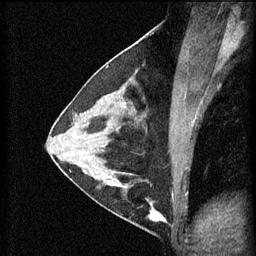
Breast MRI (dynamic contrast-enhanced), one sagittal slice; position 31 of 60 along the scan axis; 3 images stored at this slice position (order not interpretable as contrast timing); 1.5 T; TE 4.2 ms, TR 11 ms; 2 mm slice thickness; 256 × 256 image matrix, field of view 180 × 180 mm. Patient: female, 29 years.
Structures marked on this image (semi-automatic segmentation, software-assisted and operator-edited):
- analysis volume of interest (the breast-tissue region the enhancement analysis was run in; not a lesion): bounding box (x1, y1, x2, y2) in pixels: (105, 172, 168, 227)
- tumour enhancement mask (voxels above the 70 % enhancement threshold inside the analysis volume of interest): (108, 174, 168, 223)